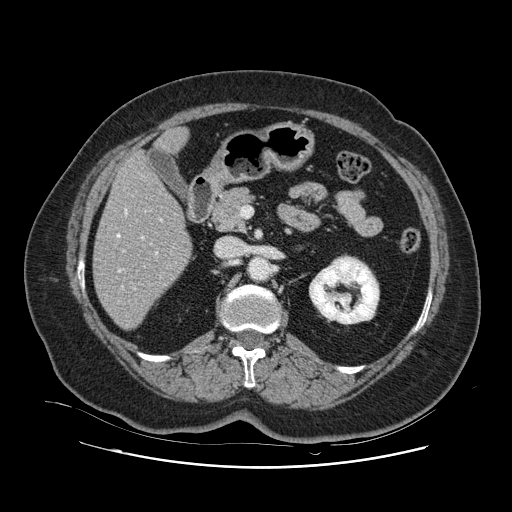
Contrast-enhanced abdominal CT, one axial slice. Position 46 of 132 along the scan axis. 120 kVp. Soft-tissue window (W 400 / L 40 HU). 2.5 mm slice thickness. 512 × 512 image matrix, field of view 391 × 391 mm. Female patient, age 73 years. Case-level facts recorded for this patient, not image findings: diagnosis: colorectal cancer liver metastases, imaged before liver resection; multiple liver metastases: no; largest metastasis: 7 cm; disease in both lobes: no.
Structures marked on this image (outlined manually by an expert reader):
- hepatic veins: box from (x=117, y=210) to (x=158, y=289) px
- liver: (x=94, y=130)–(x=192, y=329)
- planned liver remnant (the part of the liver to remain after resection): (x=95, y=156)–(x=192, y=329)
- portal vein (with intrahepatic branches): (x=133, y=219)–(x=162, y=289)